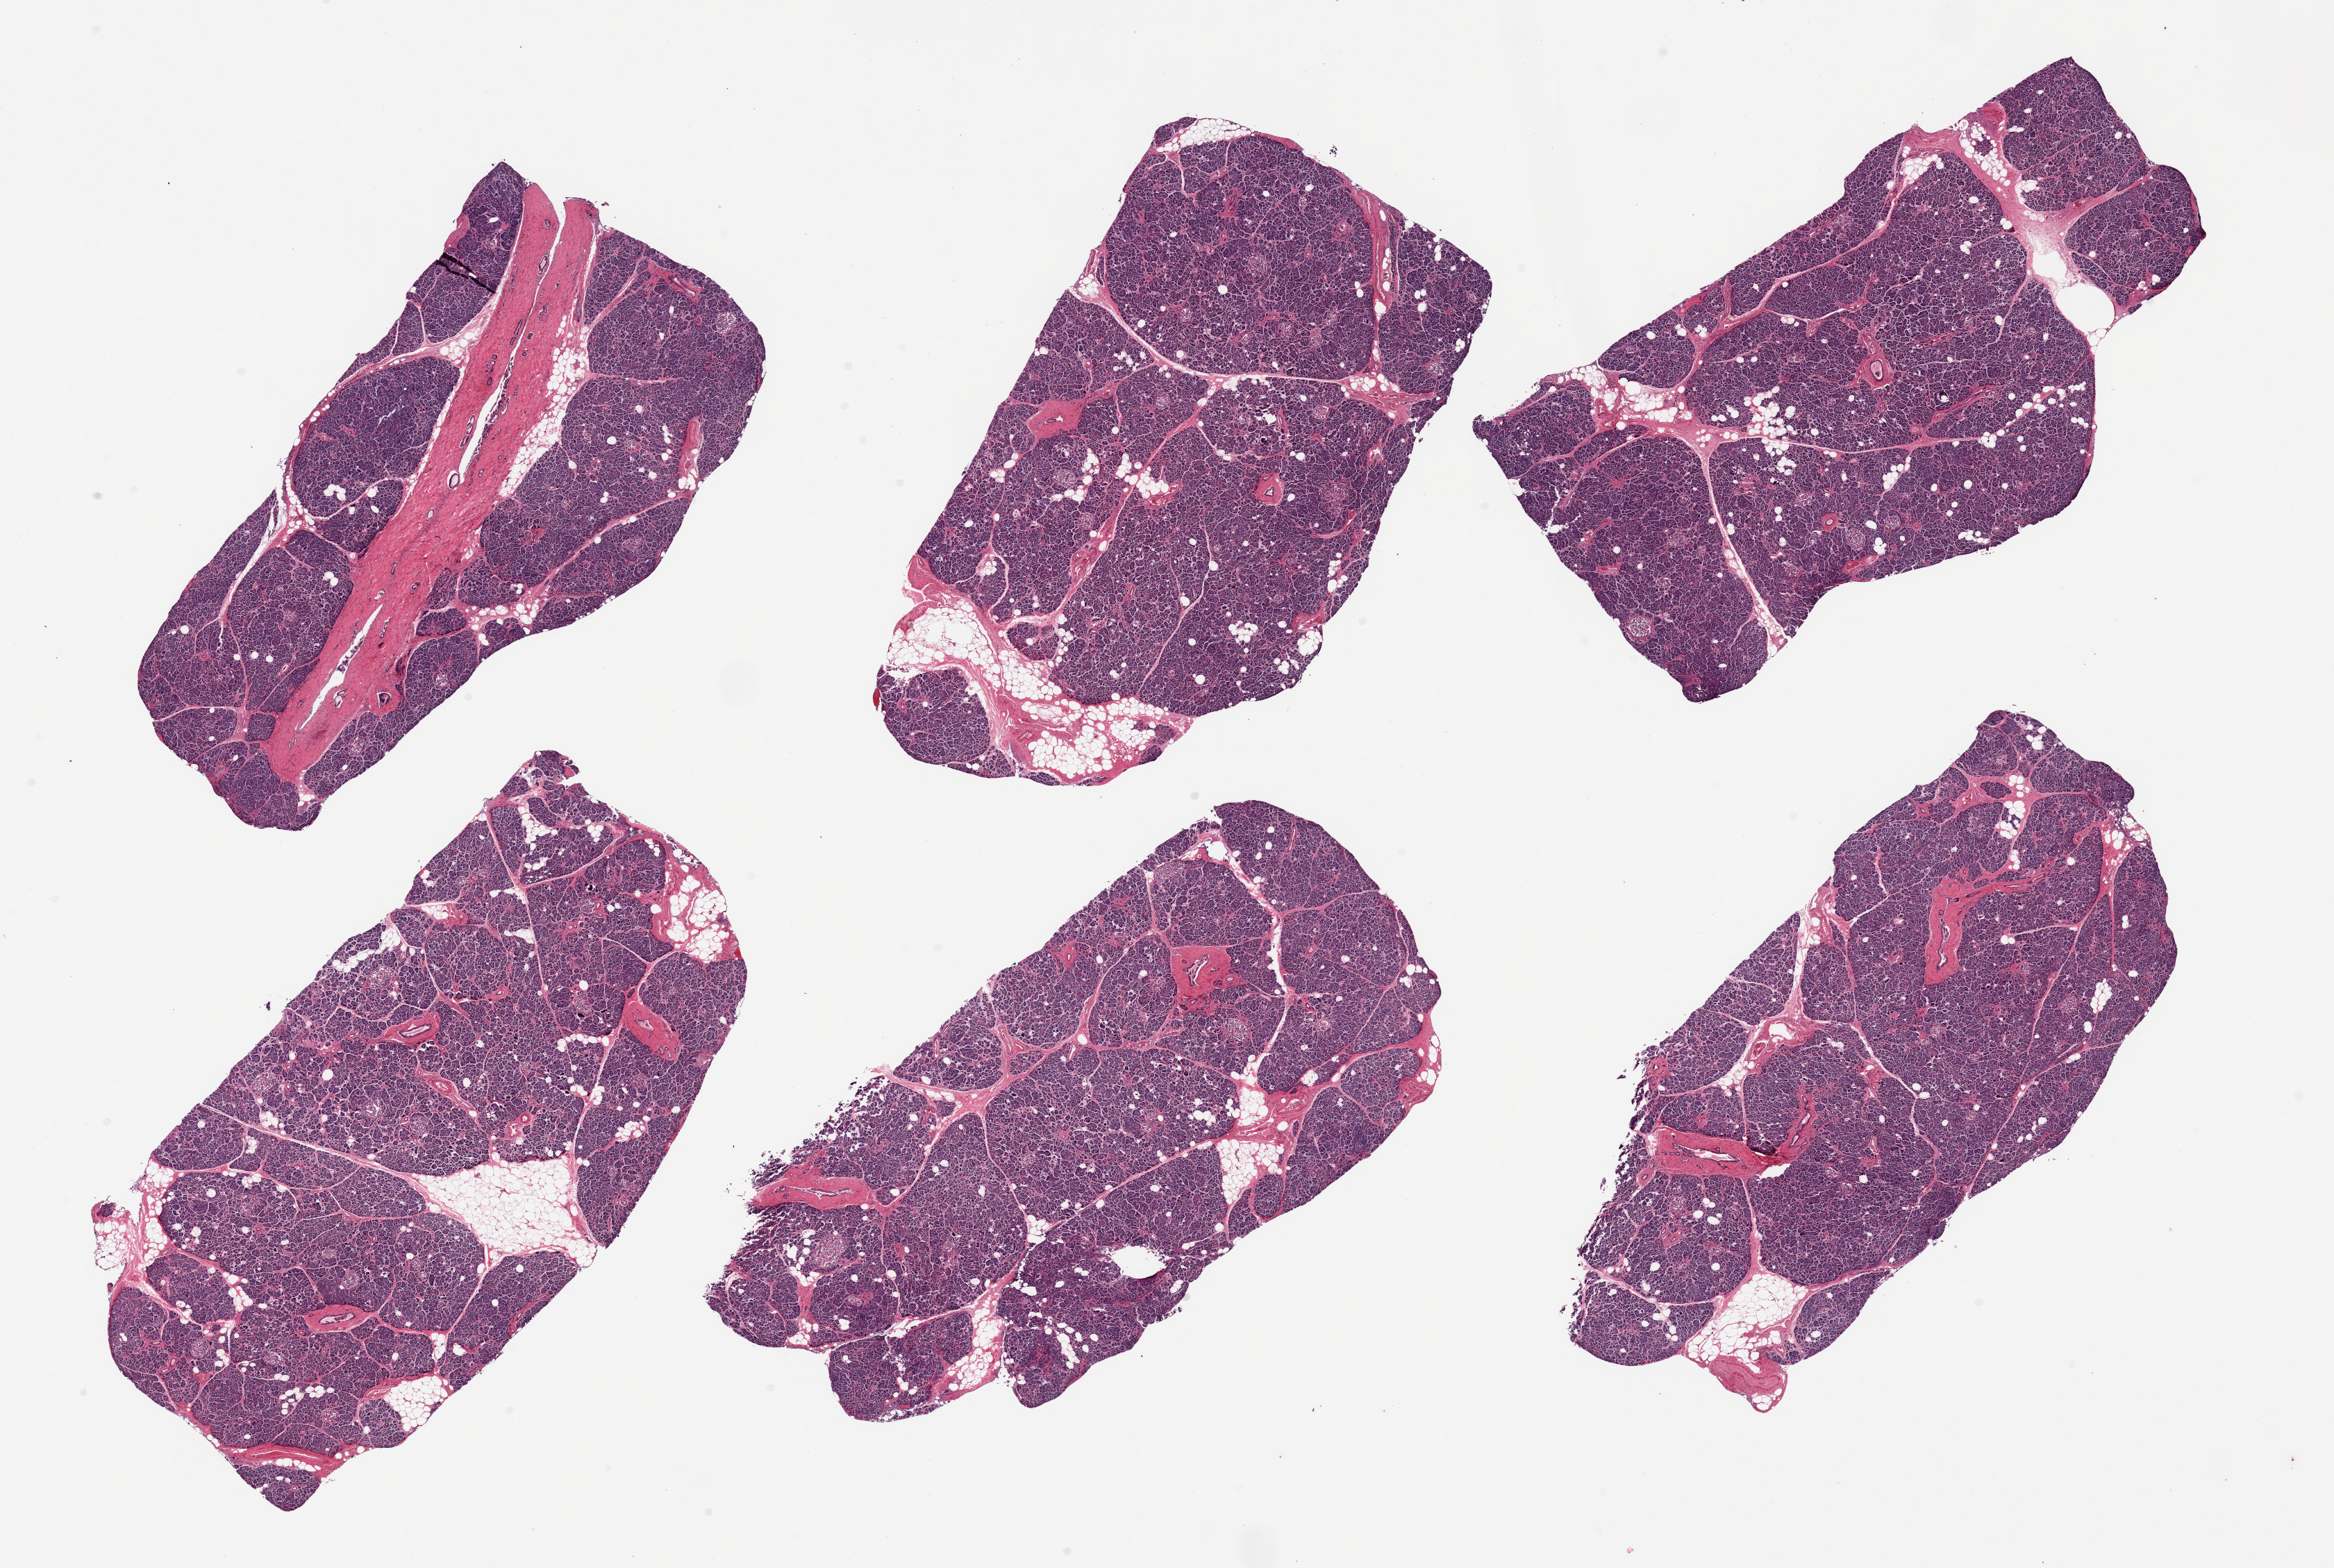
Whole-slide image, hematoxylin and eosin (H&E) stain, brightfield, whole scanned area (about 26.6 x 17.9 mm) shown as a low-resolution overview. PAXgene-fixed paraffin-embedded (PFPE) section. Sampled site (target tissue): pancreas. Donor tissue sample. Donor: male.
Review note (as recorded): 6 pieces; well preserved with ~5-10% internal fat and numerous islets.